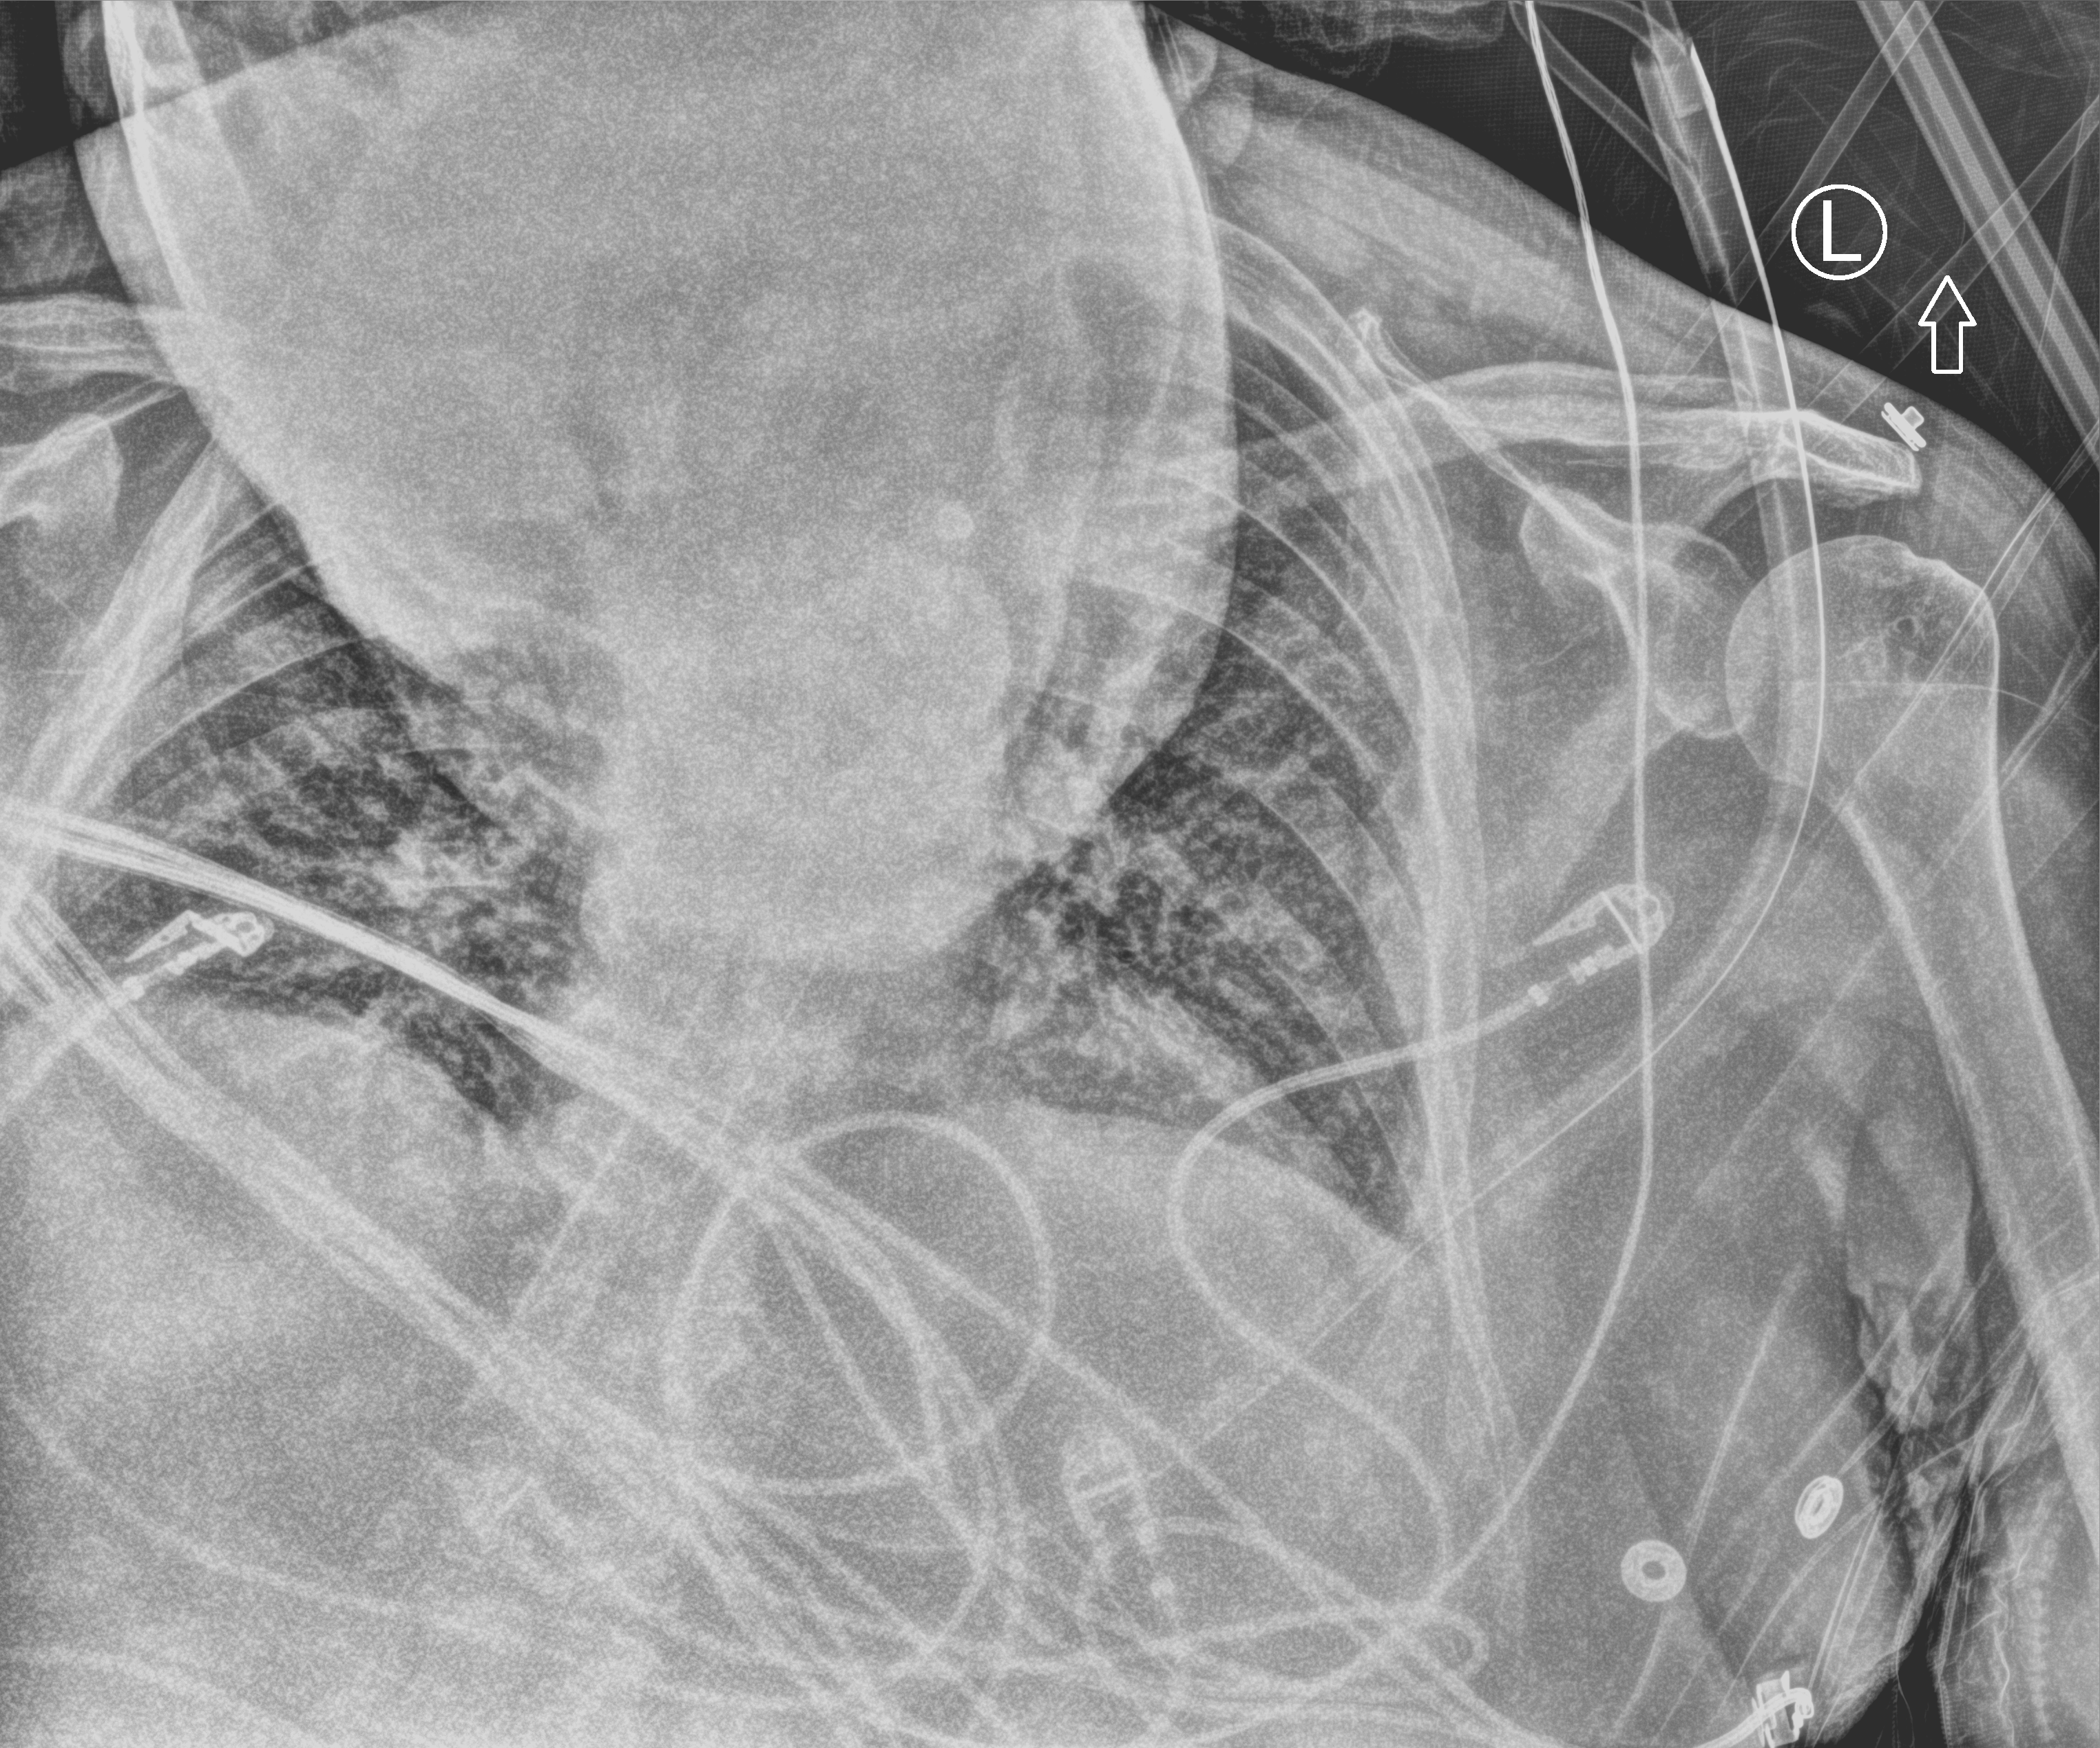
Portable chest radiograph. Patient hospitalised with COVID-19; male, aged 60–74 years.
Hospital-stay facts (about this admission, not read from this image; timing relative to this image not recorded): hypertension (admission record): yes; admitted to intensive care during this hospital stay: yes; mechanically ventilated during this hospital stay: yes.